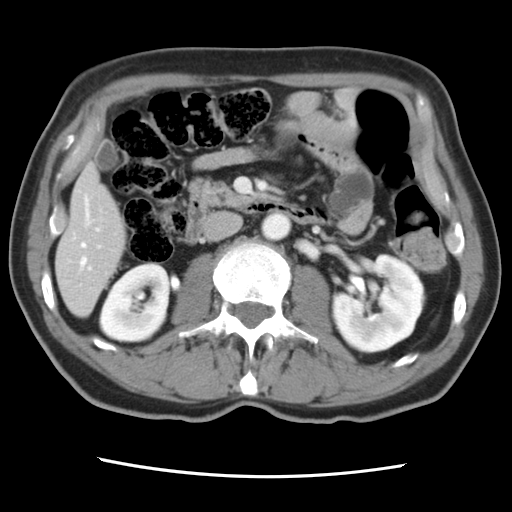
Contrast-enhanced abdominal CT, one axial slice. 120 kVp. Intravenous contrast given. Soft-tissue window (W 400 / L 40 HU). 5 mm slice thickness. 512 × 512 image matrix, field of view 321 × 321 mm. Male patient, age 69 years. Case-level facts recorded for this patient, not image findings: diagnosis: colorectal cancer liver metastases, imaged before liver resection; multiple liver metastases: yes; largest metastasis: 3.5 cm; disease in both lobes: no.
Structures marked on this image (manually delineated by an expert):
- hepatic veins: bounding box <81,199,100,266> (left, top, right, bottom; pixels)
- liver: <57,168,126,315>
- planned liver remnant (the part of the liver to remain after resection): <57,168,126,315>
- portal vein (with intrahepatic branches): <89,229,99,270>